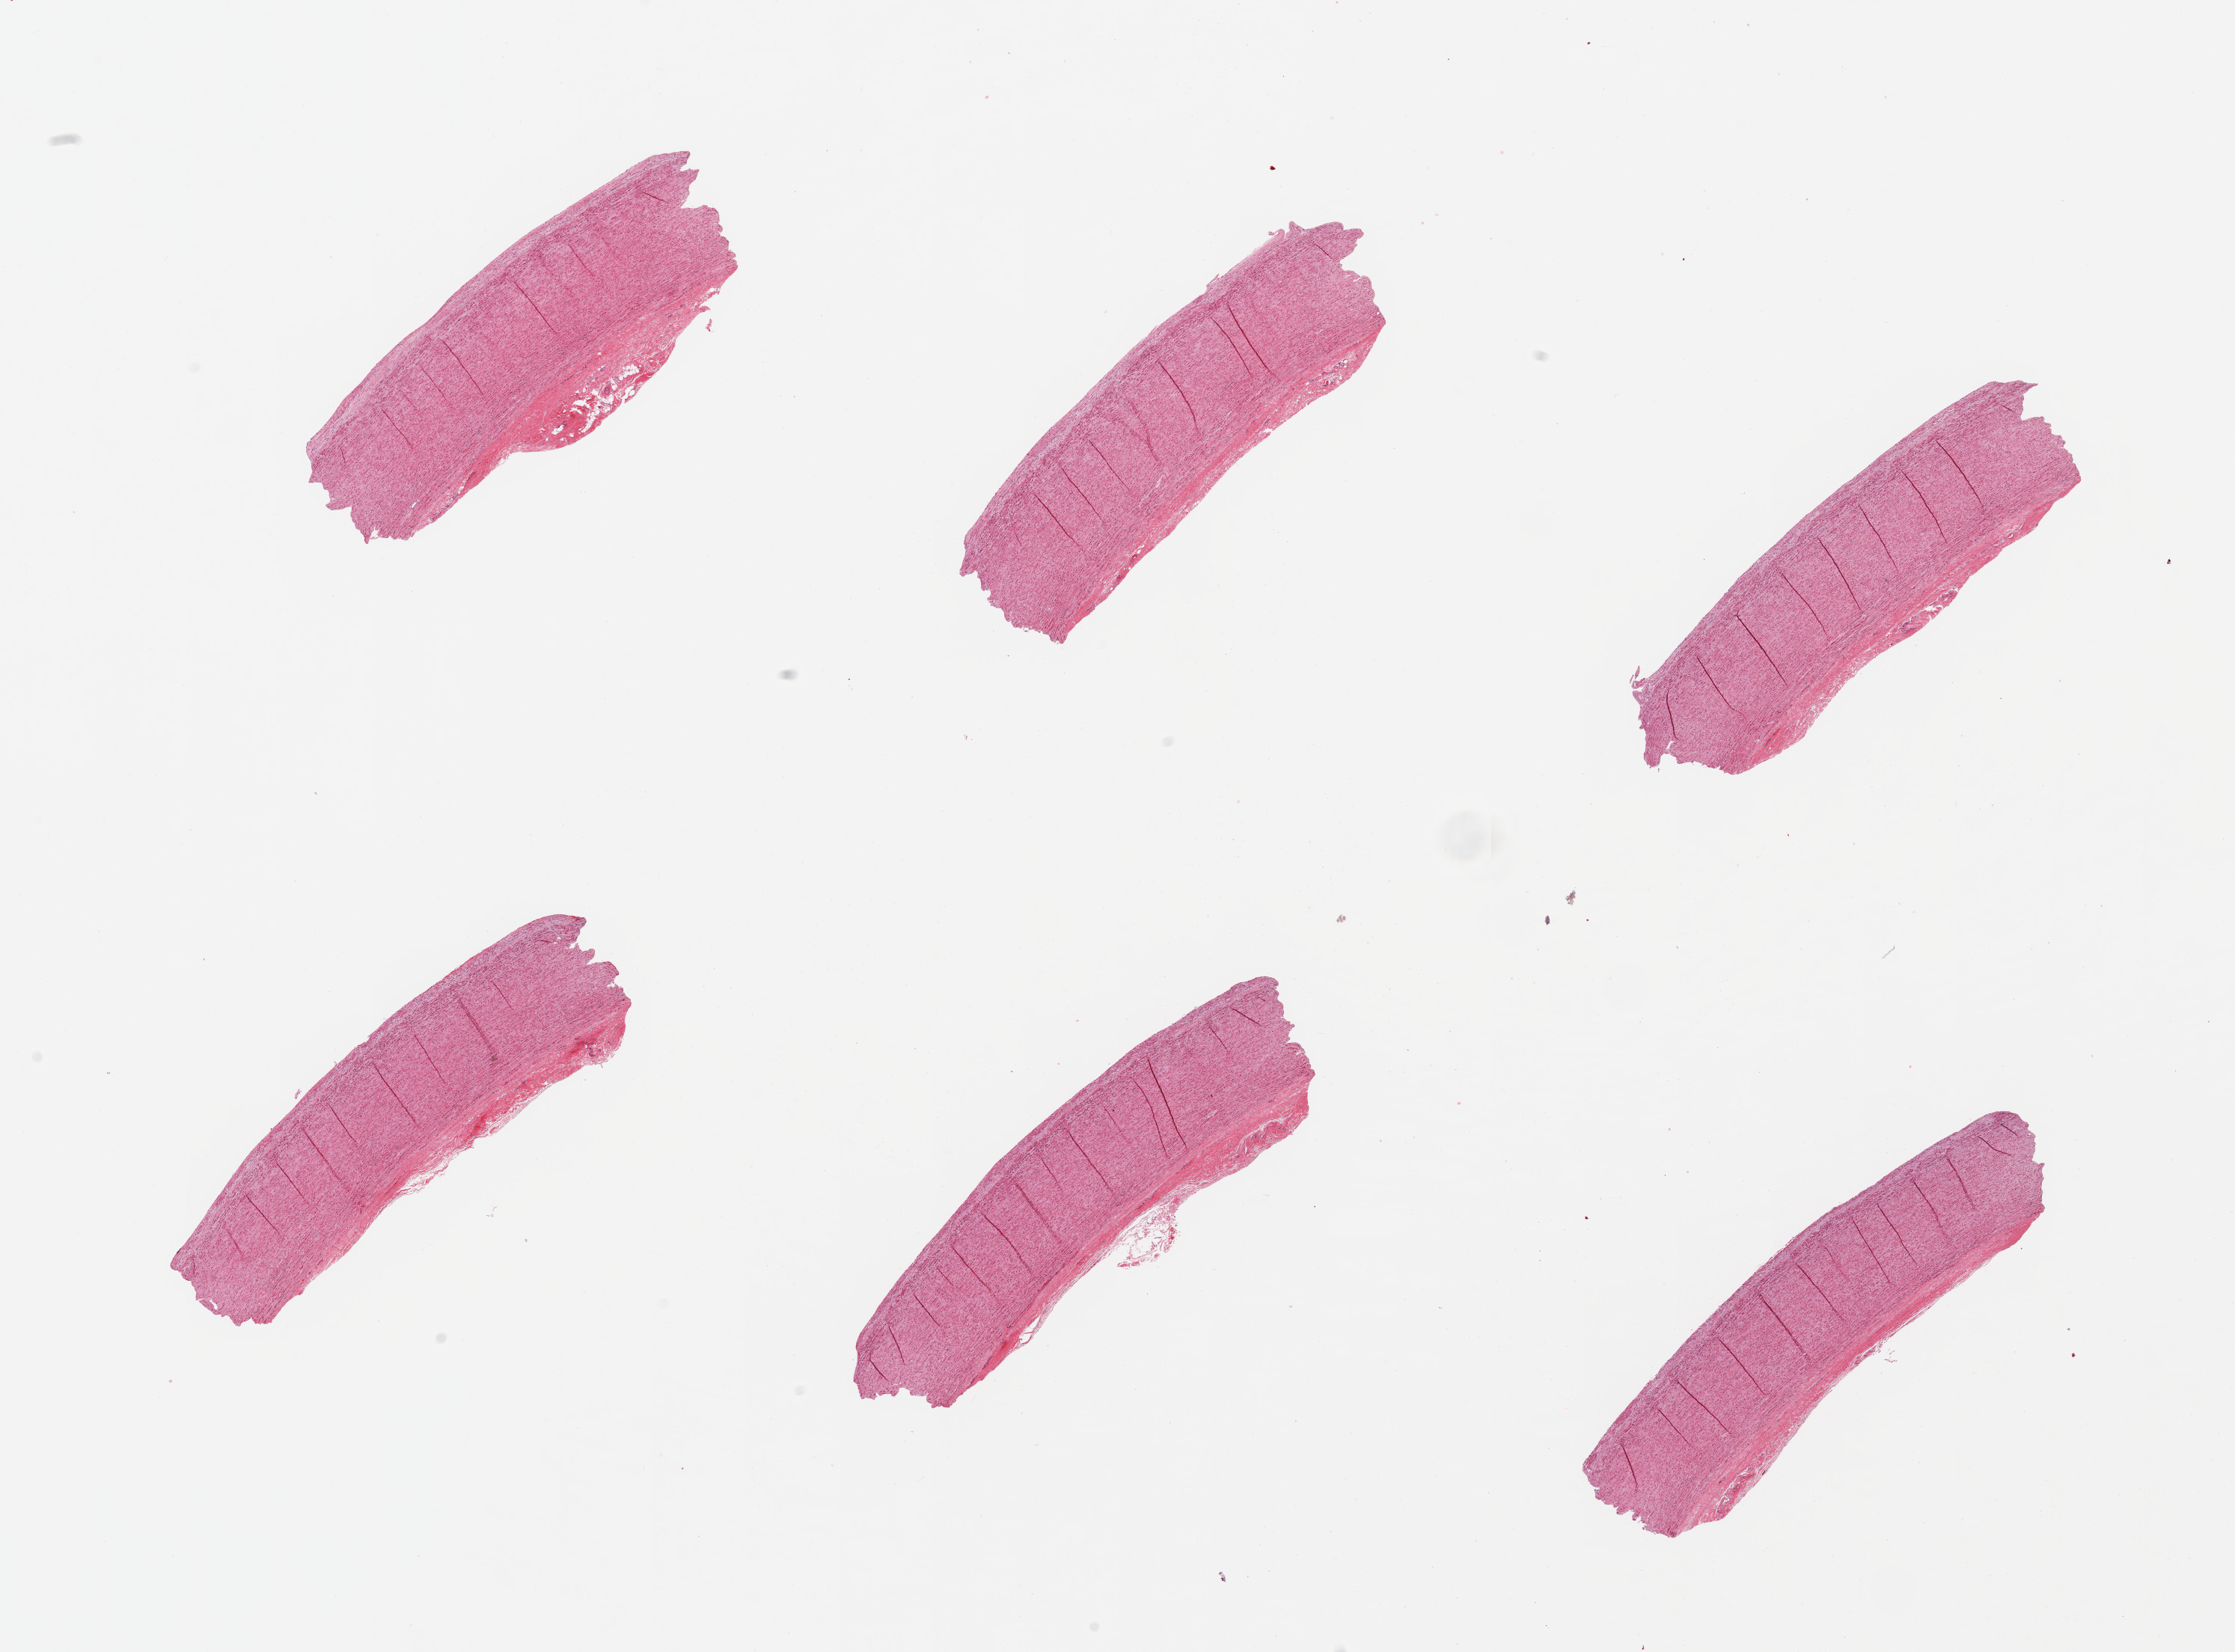
Digitized H&E-stained section, brightfield, whole scanned area (about 23.6 x 17.5 mm, from a 20x scan) shown as a low-resolution overview; PAXgene-fixed paraffin-embedded (PFPE) section; sampled site (target tissue): aorta; tissue donor sample. Donor sex: male.
Reviewer comment on this tissue sample: 6 pieces.